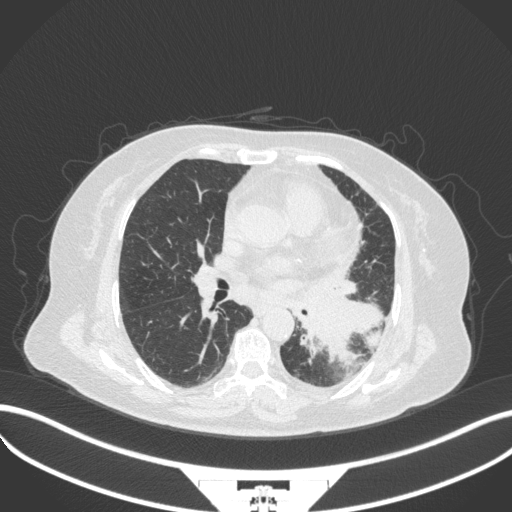
Chest CT, one axial slice. Position 177 of 328 along the scan axis. 120 kVp. Lung window (W 1500 / L -600 HU). 1 mm slice thickness. 512 × 512 image matrix, field of view 400 × 400 mm. Female patient, age 69 years. Case-level facts recorded for this patient, not image findings: clinical TNM (as recorded): T2b N3 M1.
Structures marked on this image (rectangle marked by the reading radiologist):
- lung tumour (recorded histology: adenocarcinoma): box from (x=298, y=295) to (x=383, y=360) px